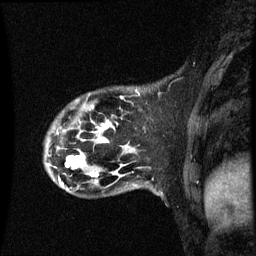
Breast MRI (dynamic contrast-enhanced), one sagittal slice. Position 14 of 60 along the scan axis. Dynamic contrast-enhanced series, image 2 of 3 at this slice position (ordered by acquisition). 1.5 T. TE 4.2 ms, TR 8.9 ms. 256 × 256 image matrix. Patient: female, 44 years. Case-level facts recorded for this patient, not image findings: setting: breast cancer imaged before/during neoadjuvant chemotherapy; receptor status: HR-positive, HER2-negative.
Structures marked on this image (semi-automatic segmentation, software-assisted and operator-edited):
- analysis volume of interest (the breast-tissue region the enhancement analysis was run in; not a lesion): bounding box (x1, y1, x2, y2) in pixels: (44, 90, 141, 189)
- tumour enhancement mask (voxels above the 70 % enhancement threshold inside the analysis volume of interest): (65, 124, 106, 177)